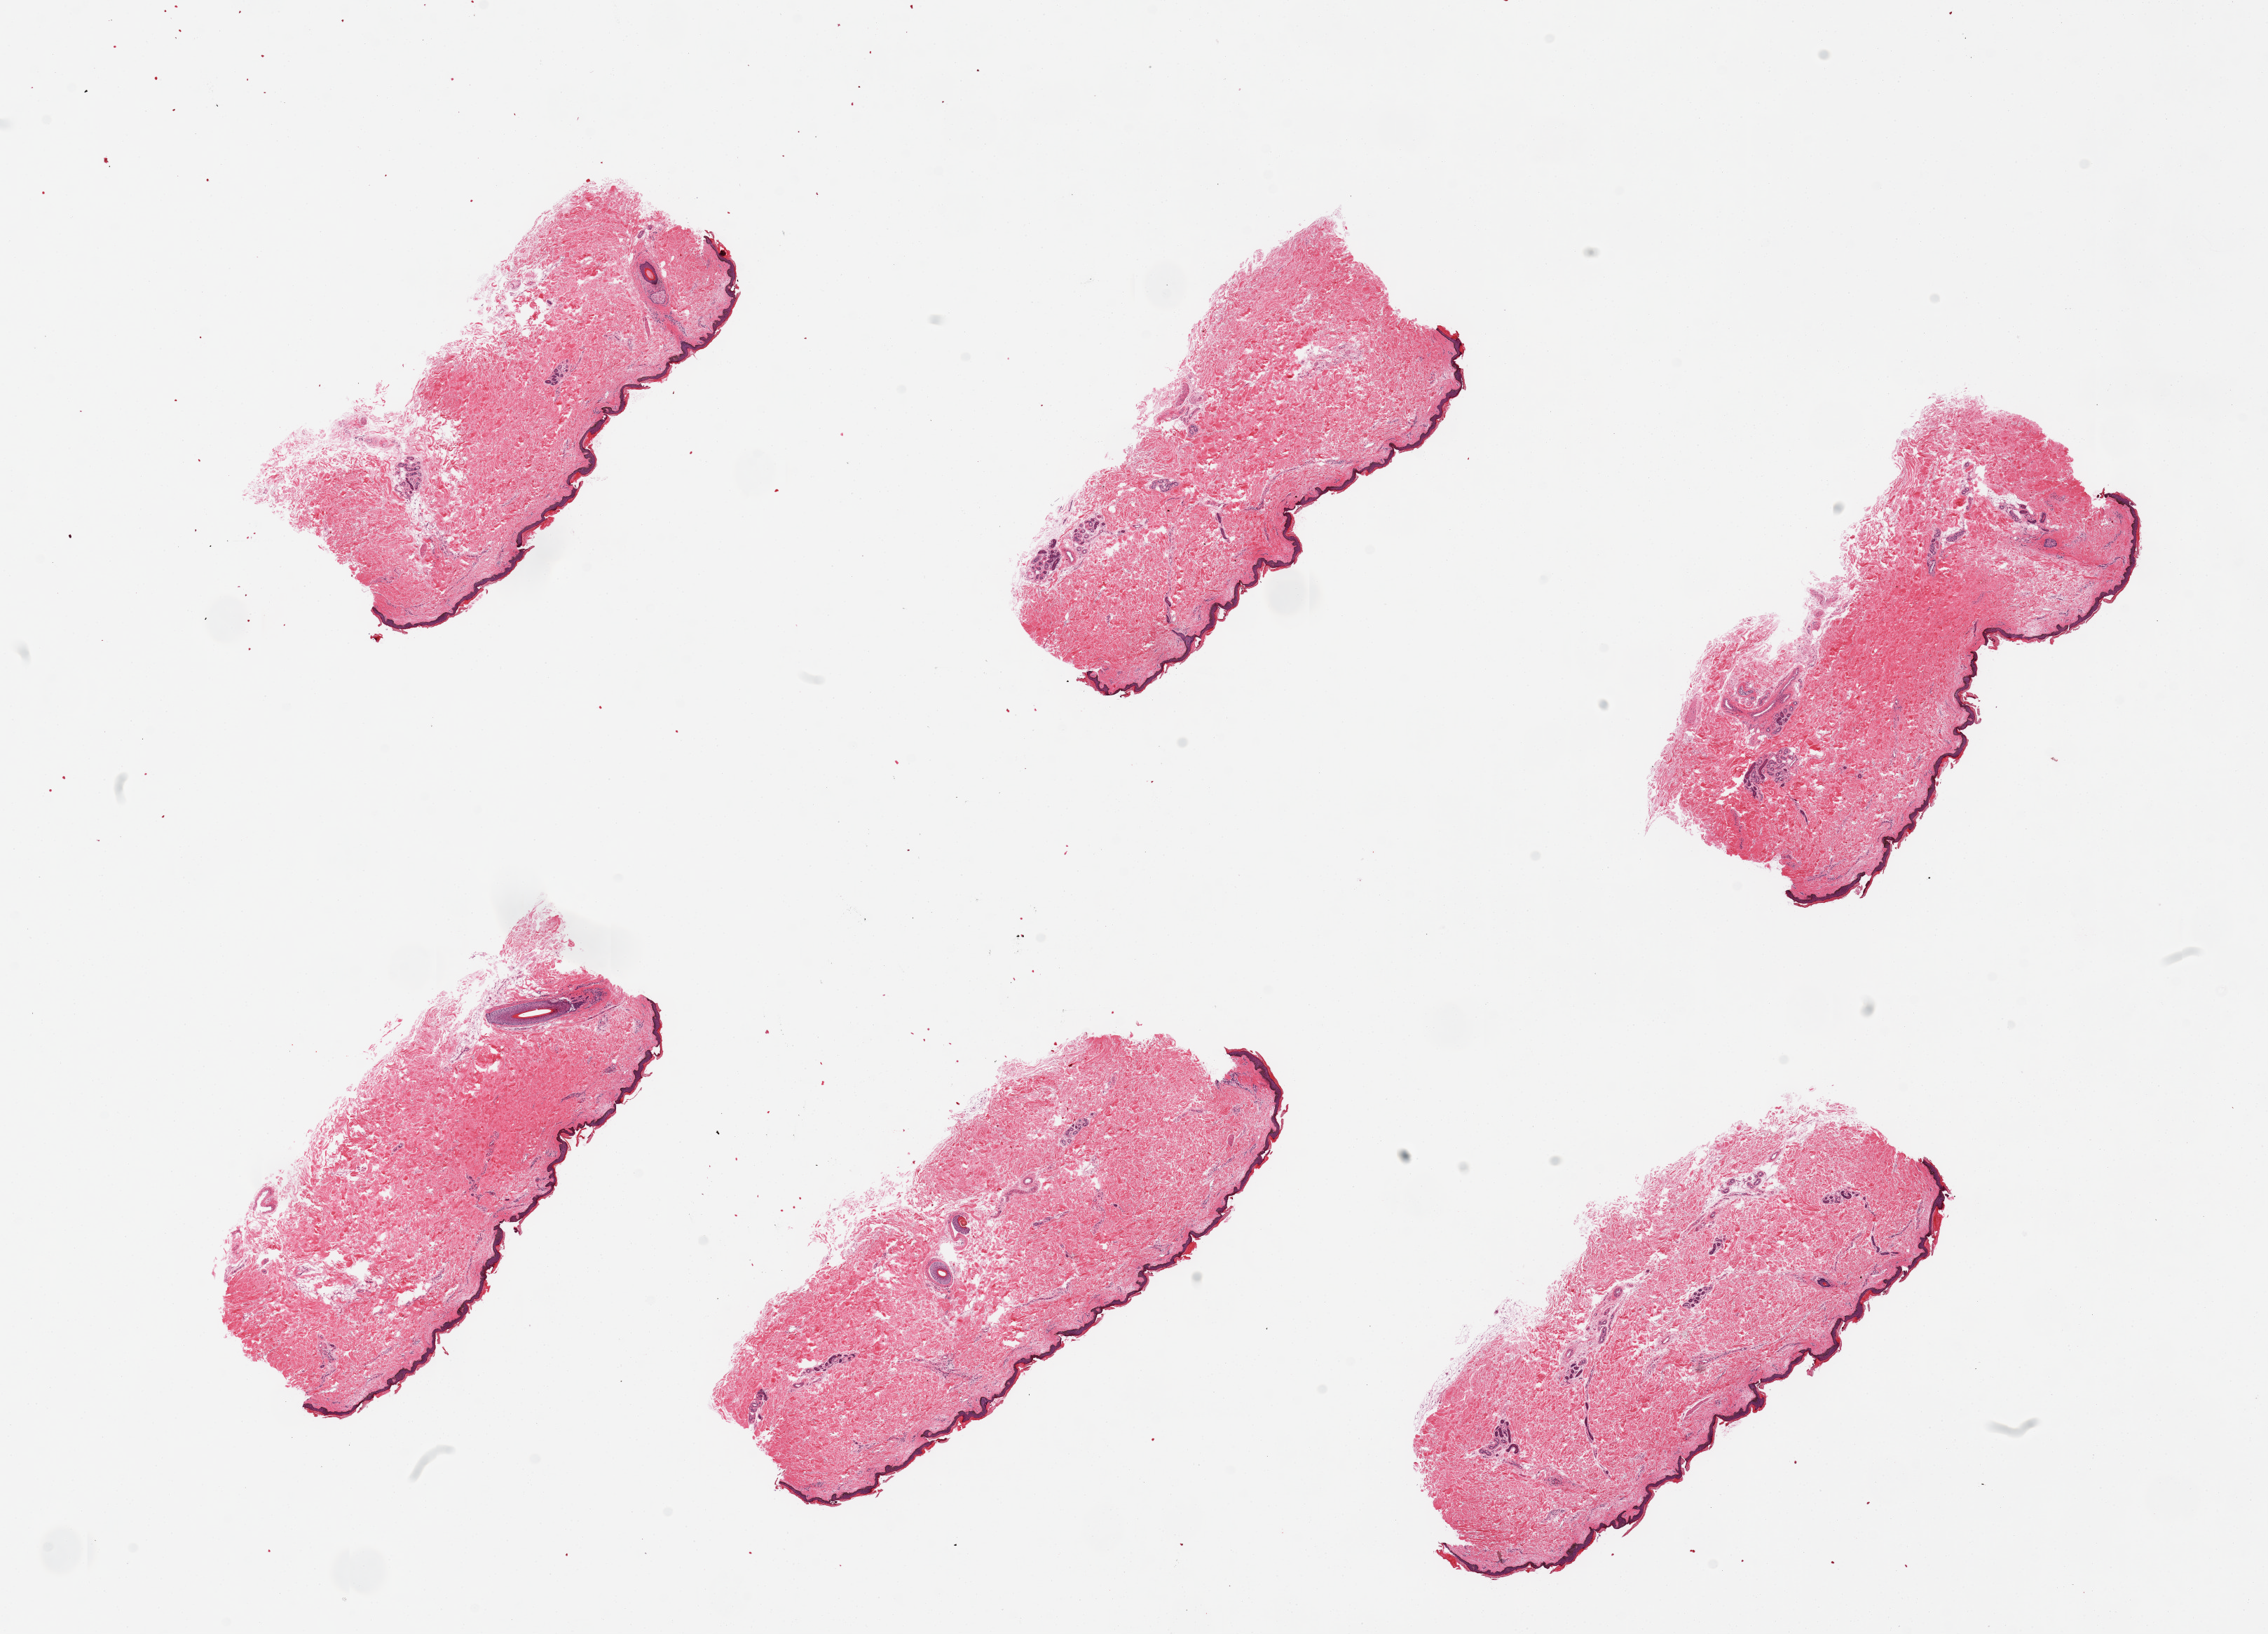
Digitized H&E-stained section — shown as a low-resolution overview of the whole scanned area (about 25.6 x 18.4 mm); PAXgene-fixed, paraffin-embedded tissue; sampled site (target tissue): skin of lower leg; tissue donor sample. Donor: male.
Pathologist's review note for this sample: 6 pieces, well trimmed, squamous epithelium measures 45-65 microns.